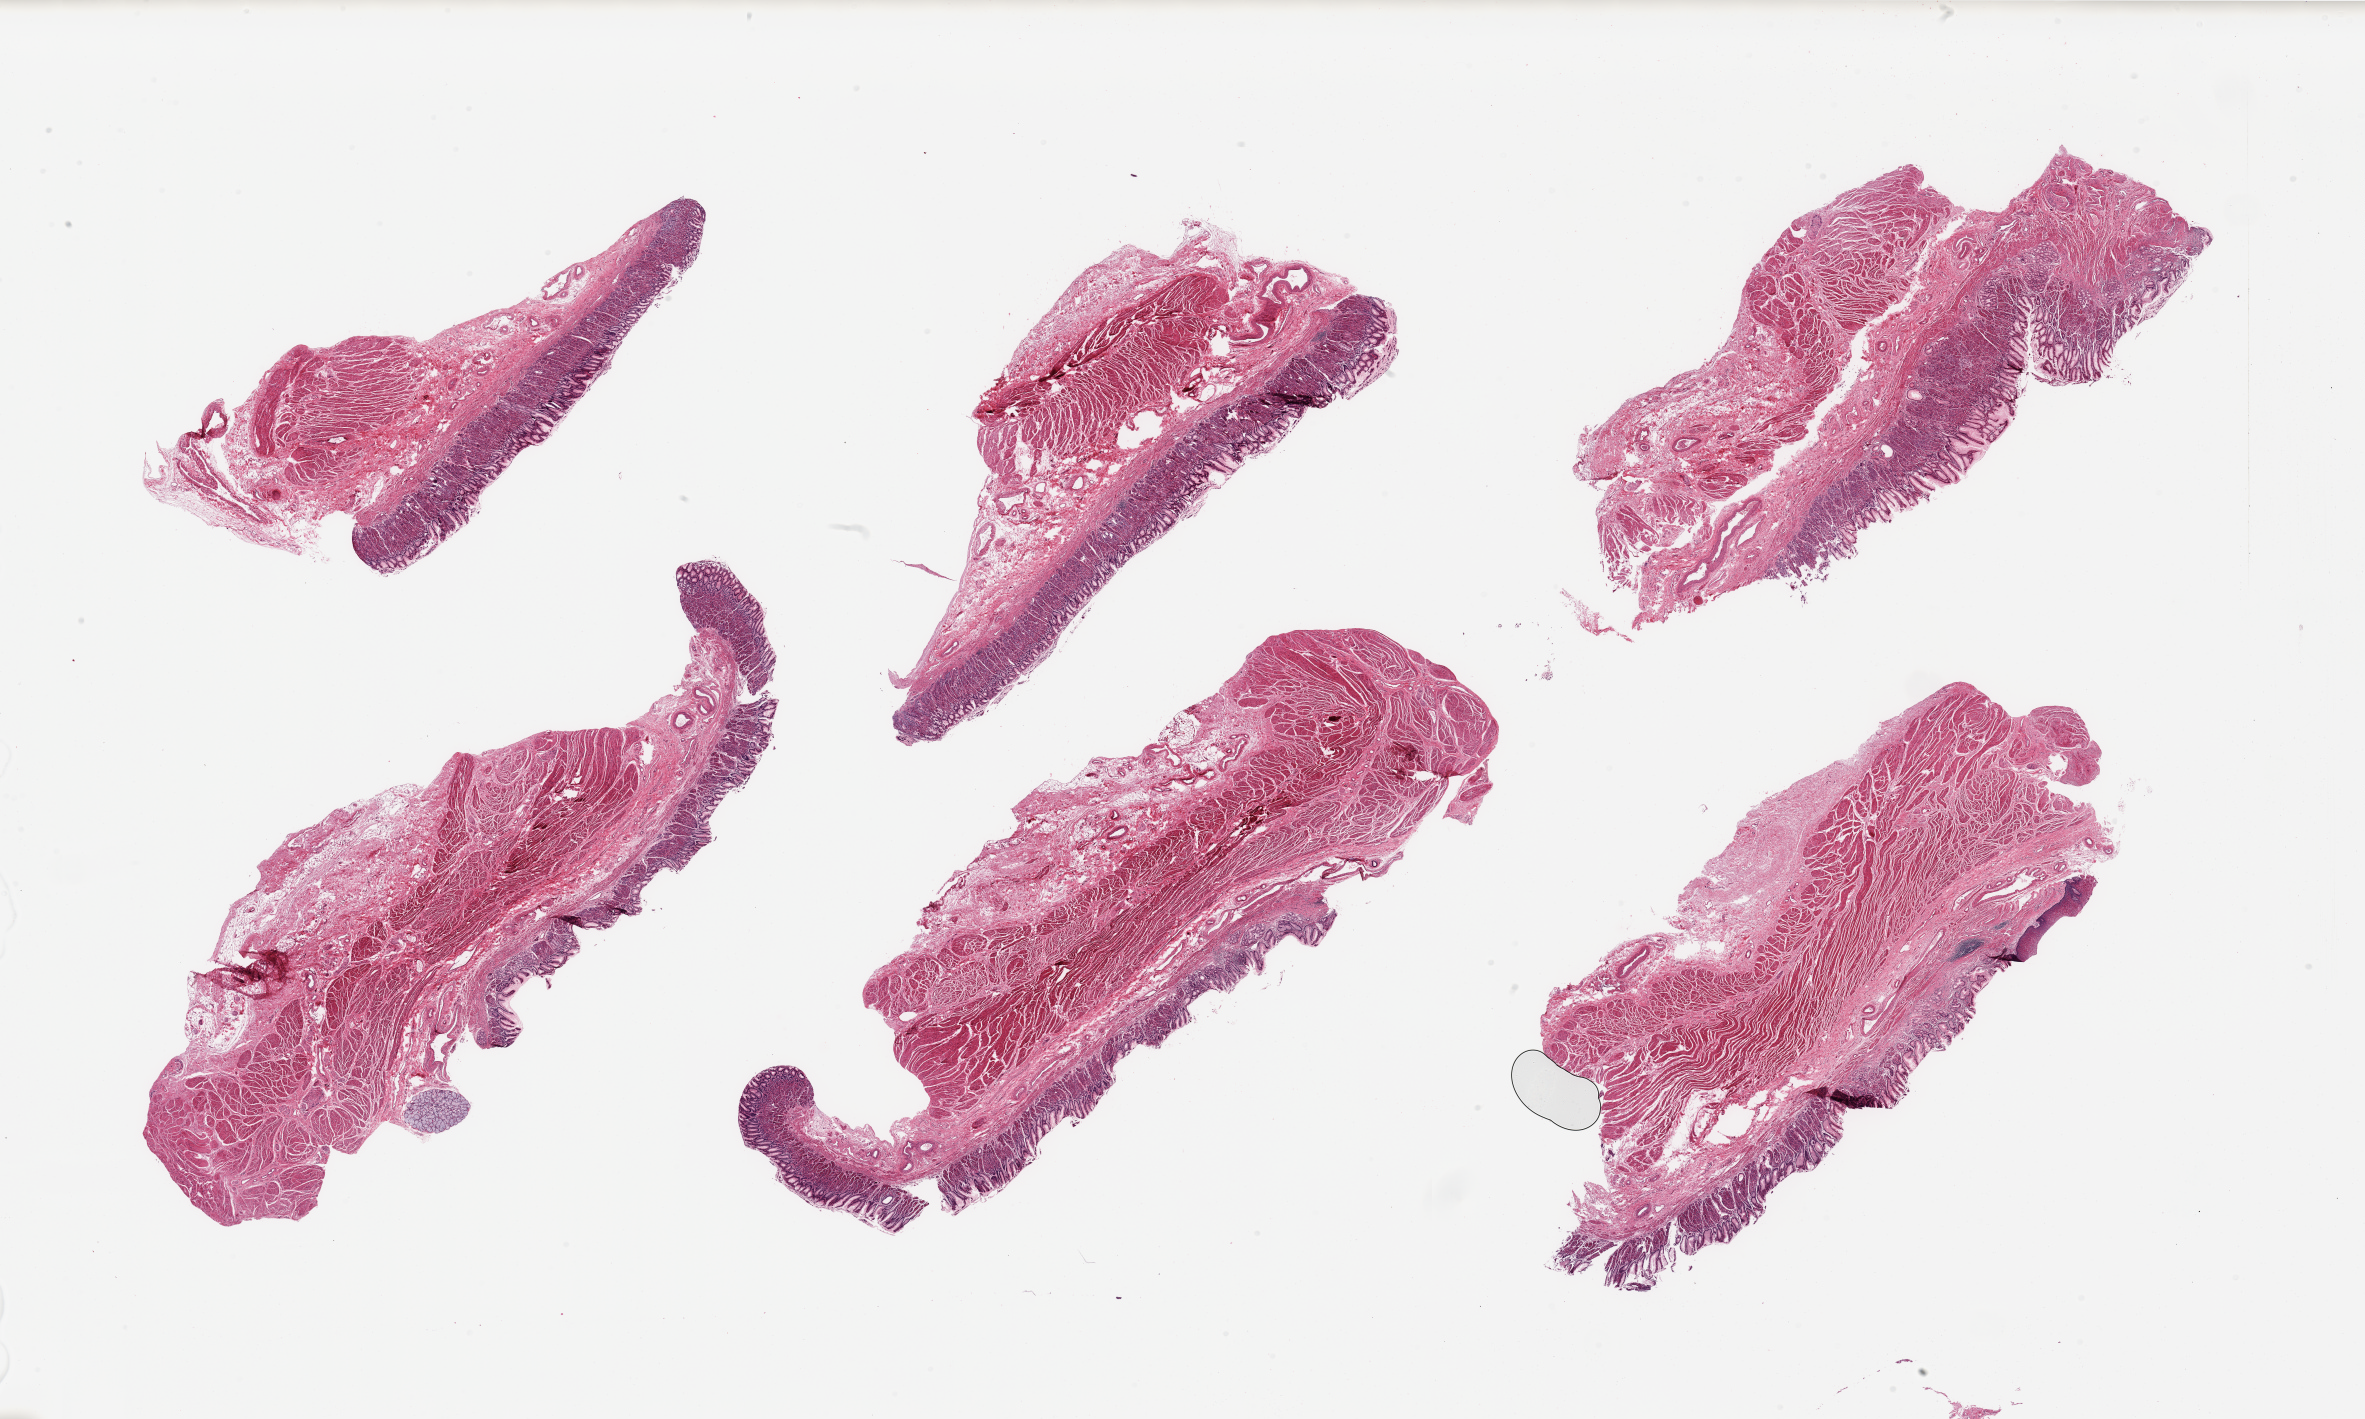
Whole-slide image, H&E stain, whole scanned area (about 37.4 x 22.4 mm) shown as a low-resolution overview, PAXgene-fixed paraffin-embedded (PFPE) section, sampled site (target tissue): gastroesophageal junction, tissue donor sample. Male donor.
Pathologist's review note for this sample: 6 pieces, target muscularis present; gastric mucosa present, wrong target source.